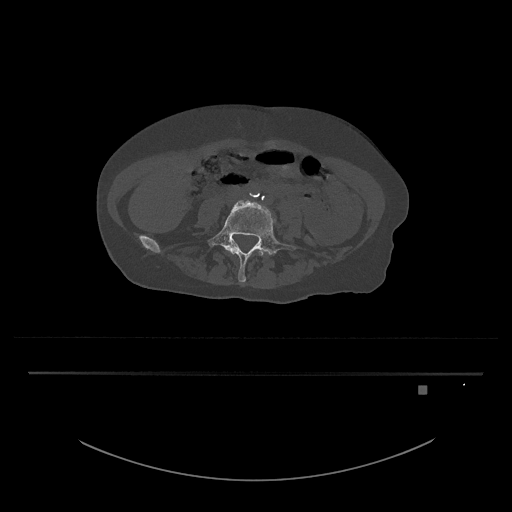
CT including the spine, one axial slice. Slice 313 of 797 in the series (ordered by position). Reconstruction kernel Br40s/3. Bone window (W 1800 / L 400 HU). 0.5 mm slice thickness. 512 × 512 image matrix. Patient: female, 57 years. From the clinical record (not read from this slice): primary cancer: cervical.
Outlined on this slice (semi-automatically segmented with operator editing):
- L4 vertebra: bounding box <230,248,264,256> (left, top, right, bottom; pixels)